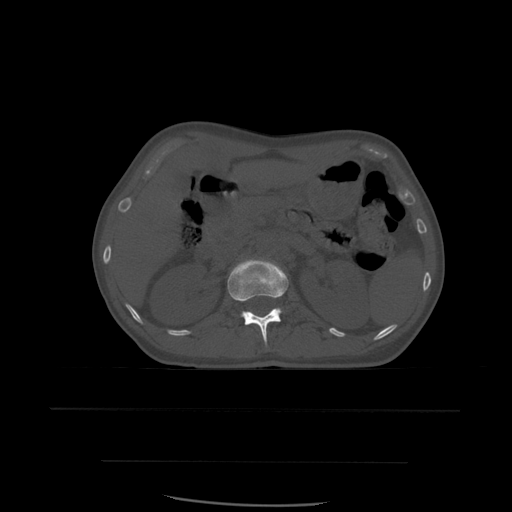
CT including the spine, one axial slice; position 247 of 574 along the scan axis; bone window (W 1800 / L 400 HU); 1.25 mm slice thickness; 512 × 512 image matrix, field of view 392 × 392 mm. Patient age 48 years. Case-level facts recorded for this patient, not image findings: primary cancer: lung; vertebrae with lytic lesions (as recorded): T11.
Outlined on this slice (semi-automatic segmentation, software-assisted and operator-edited):
- L1 vertebra: box from (x=228, y=259) to (x=289, y=345) px